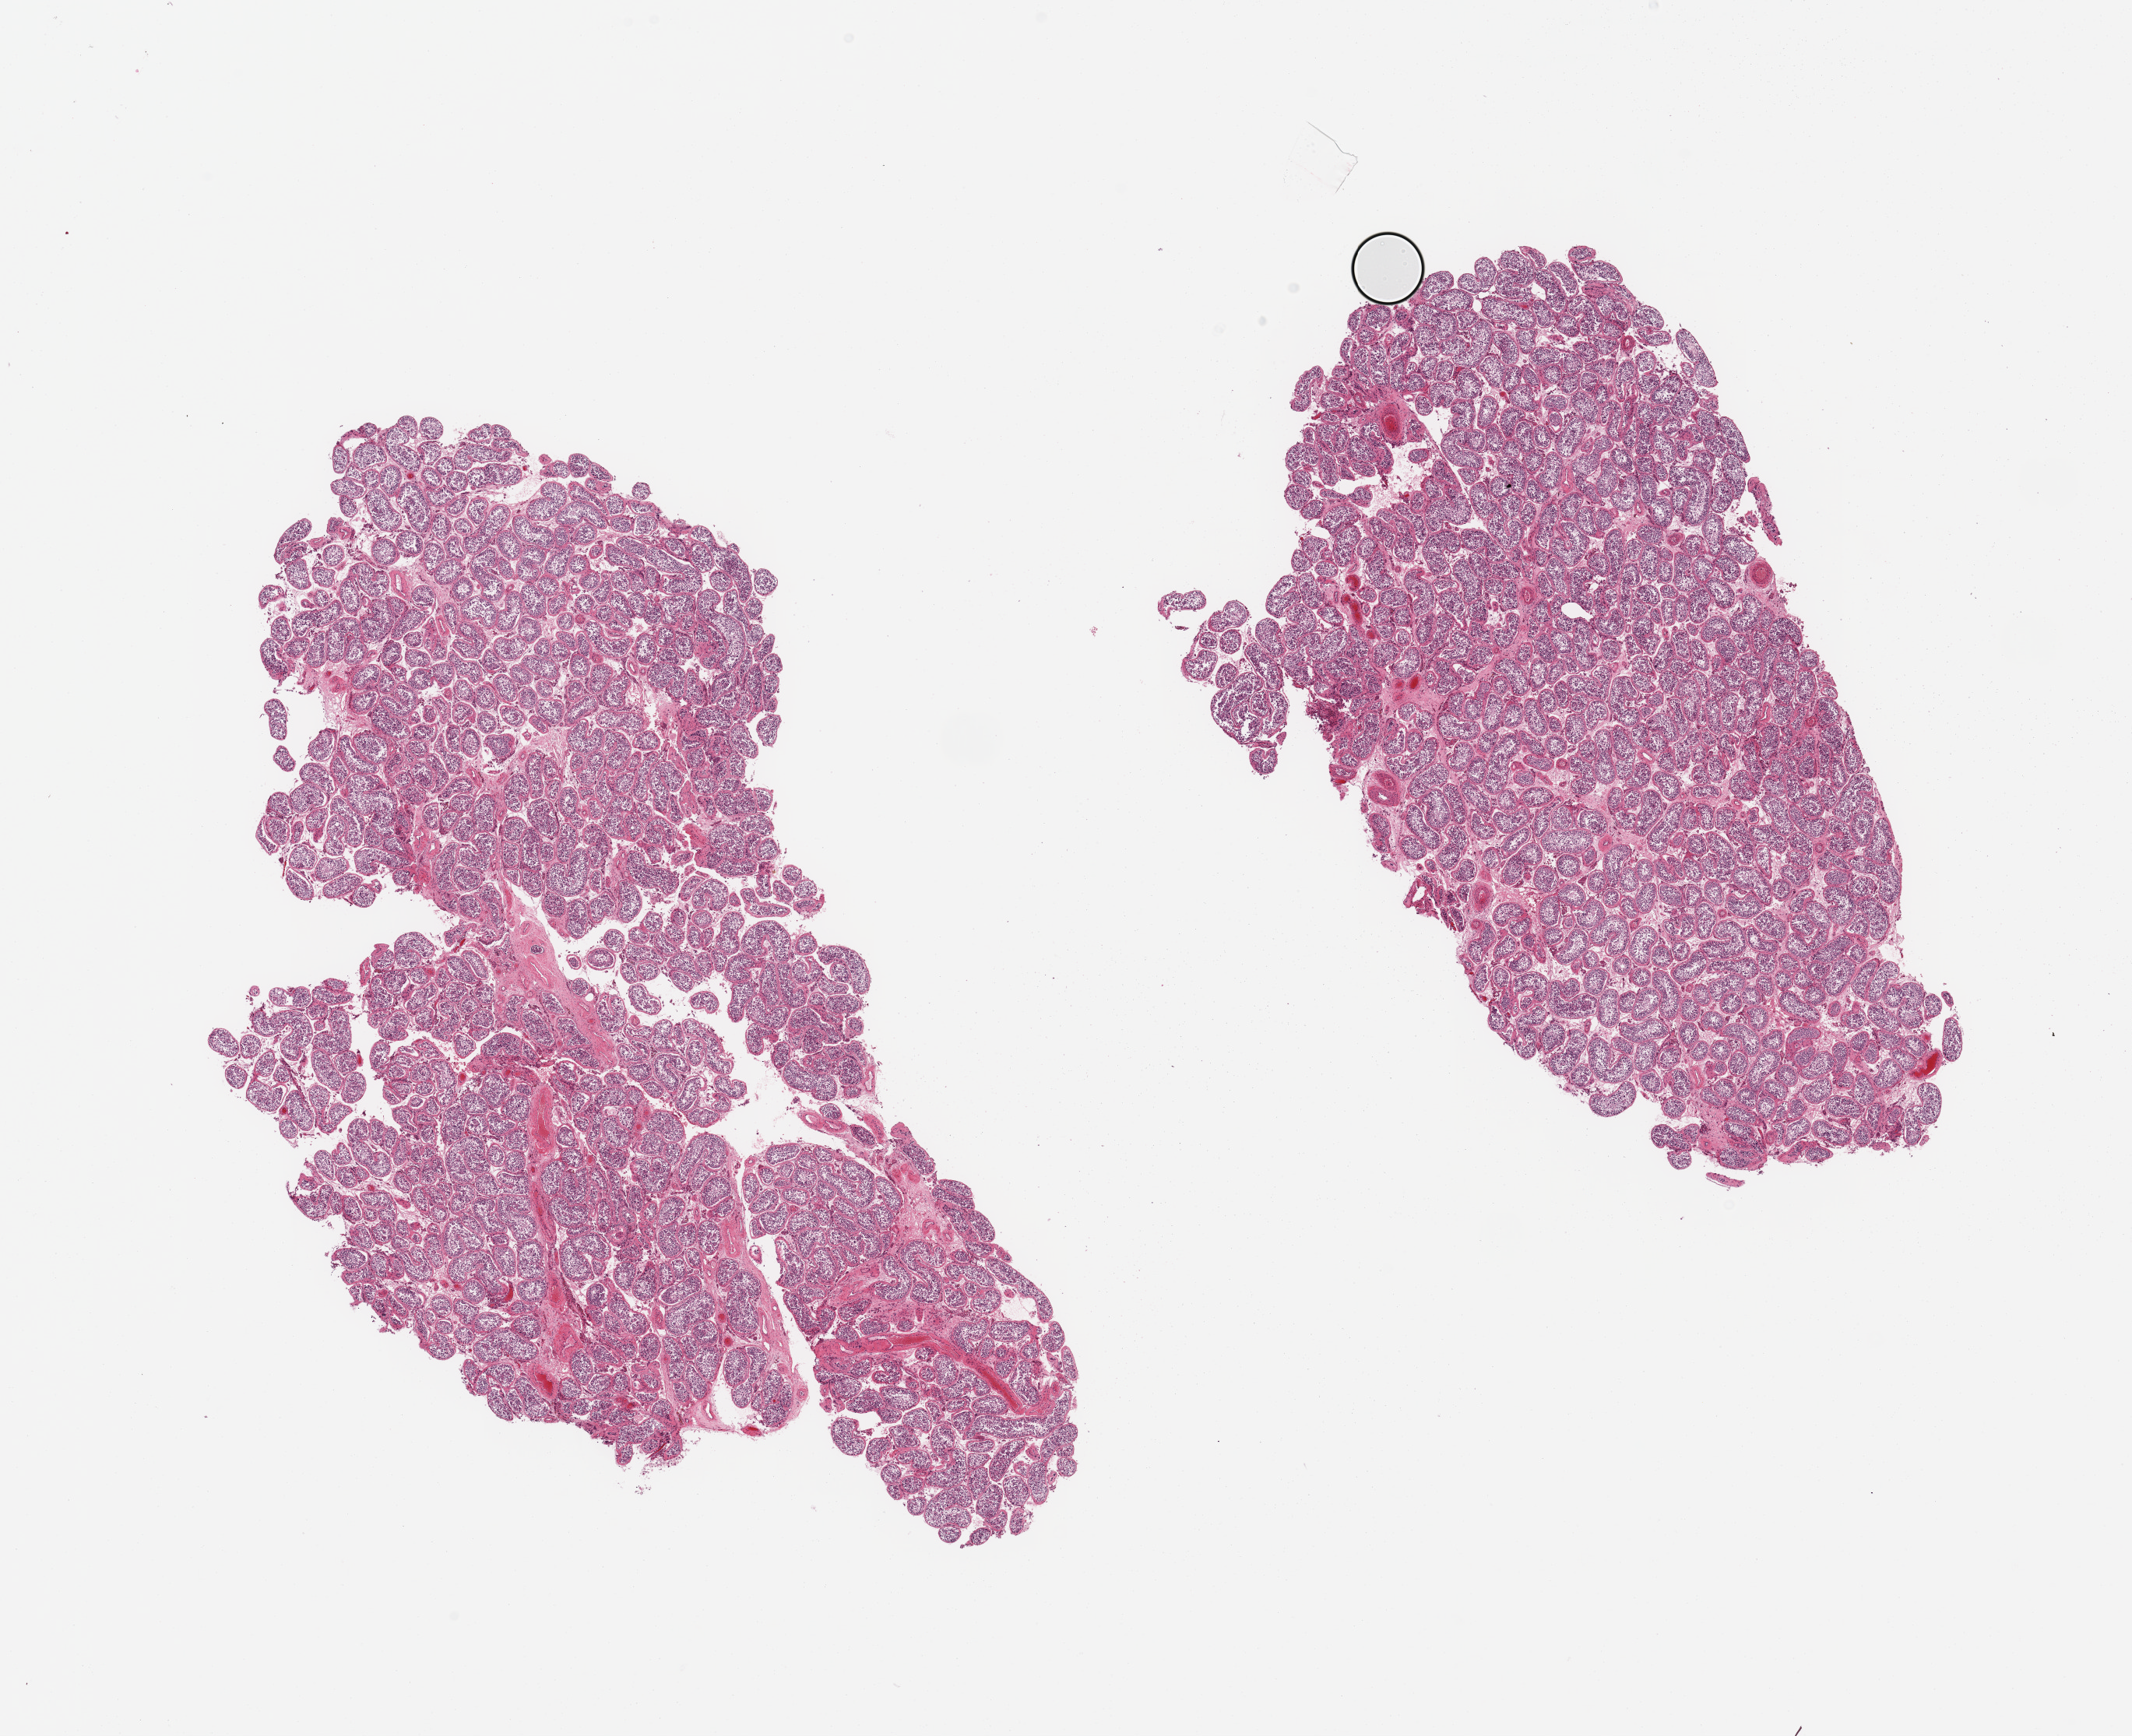
Haematoxylin and eosin whole-slide image — a low-resolution overview of the entire scanned area, about 21.7 x 17.6 mm (from a 20x scan). PAXgene-fixed, paraffin-embedded tissue. Target tissue: testis. Donor tissue sample. Male donor.
Pathologist's review note for this sample: 2 pieces; spermatogenesis present; congestion.